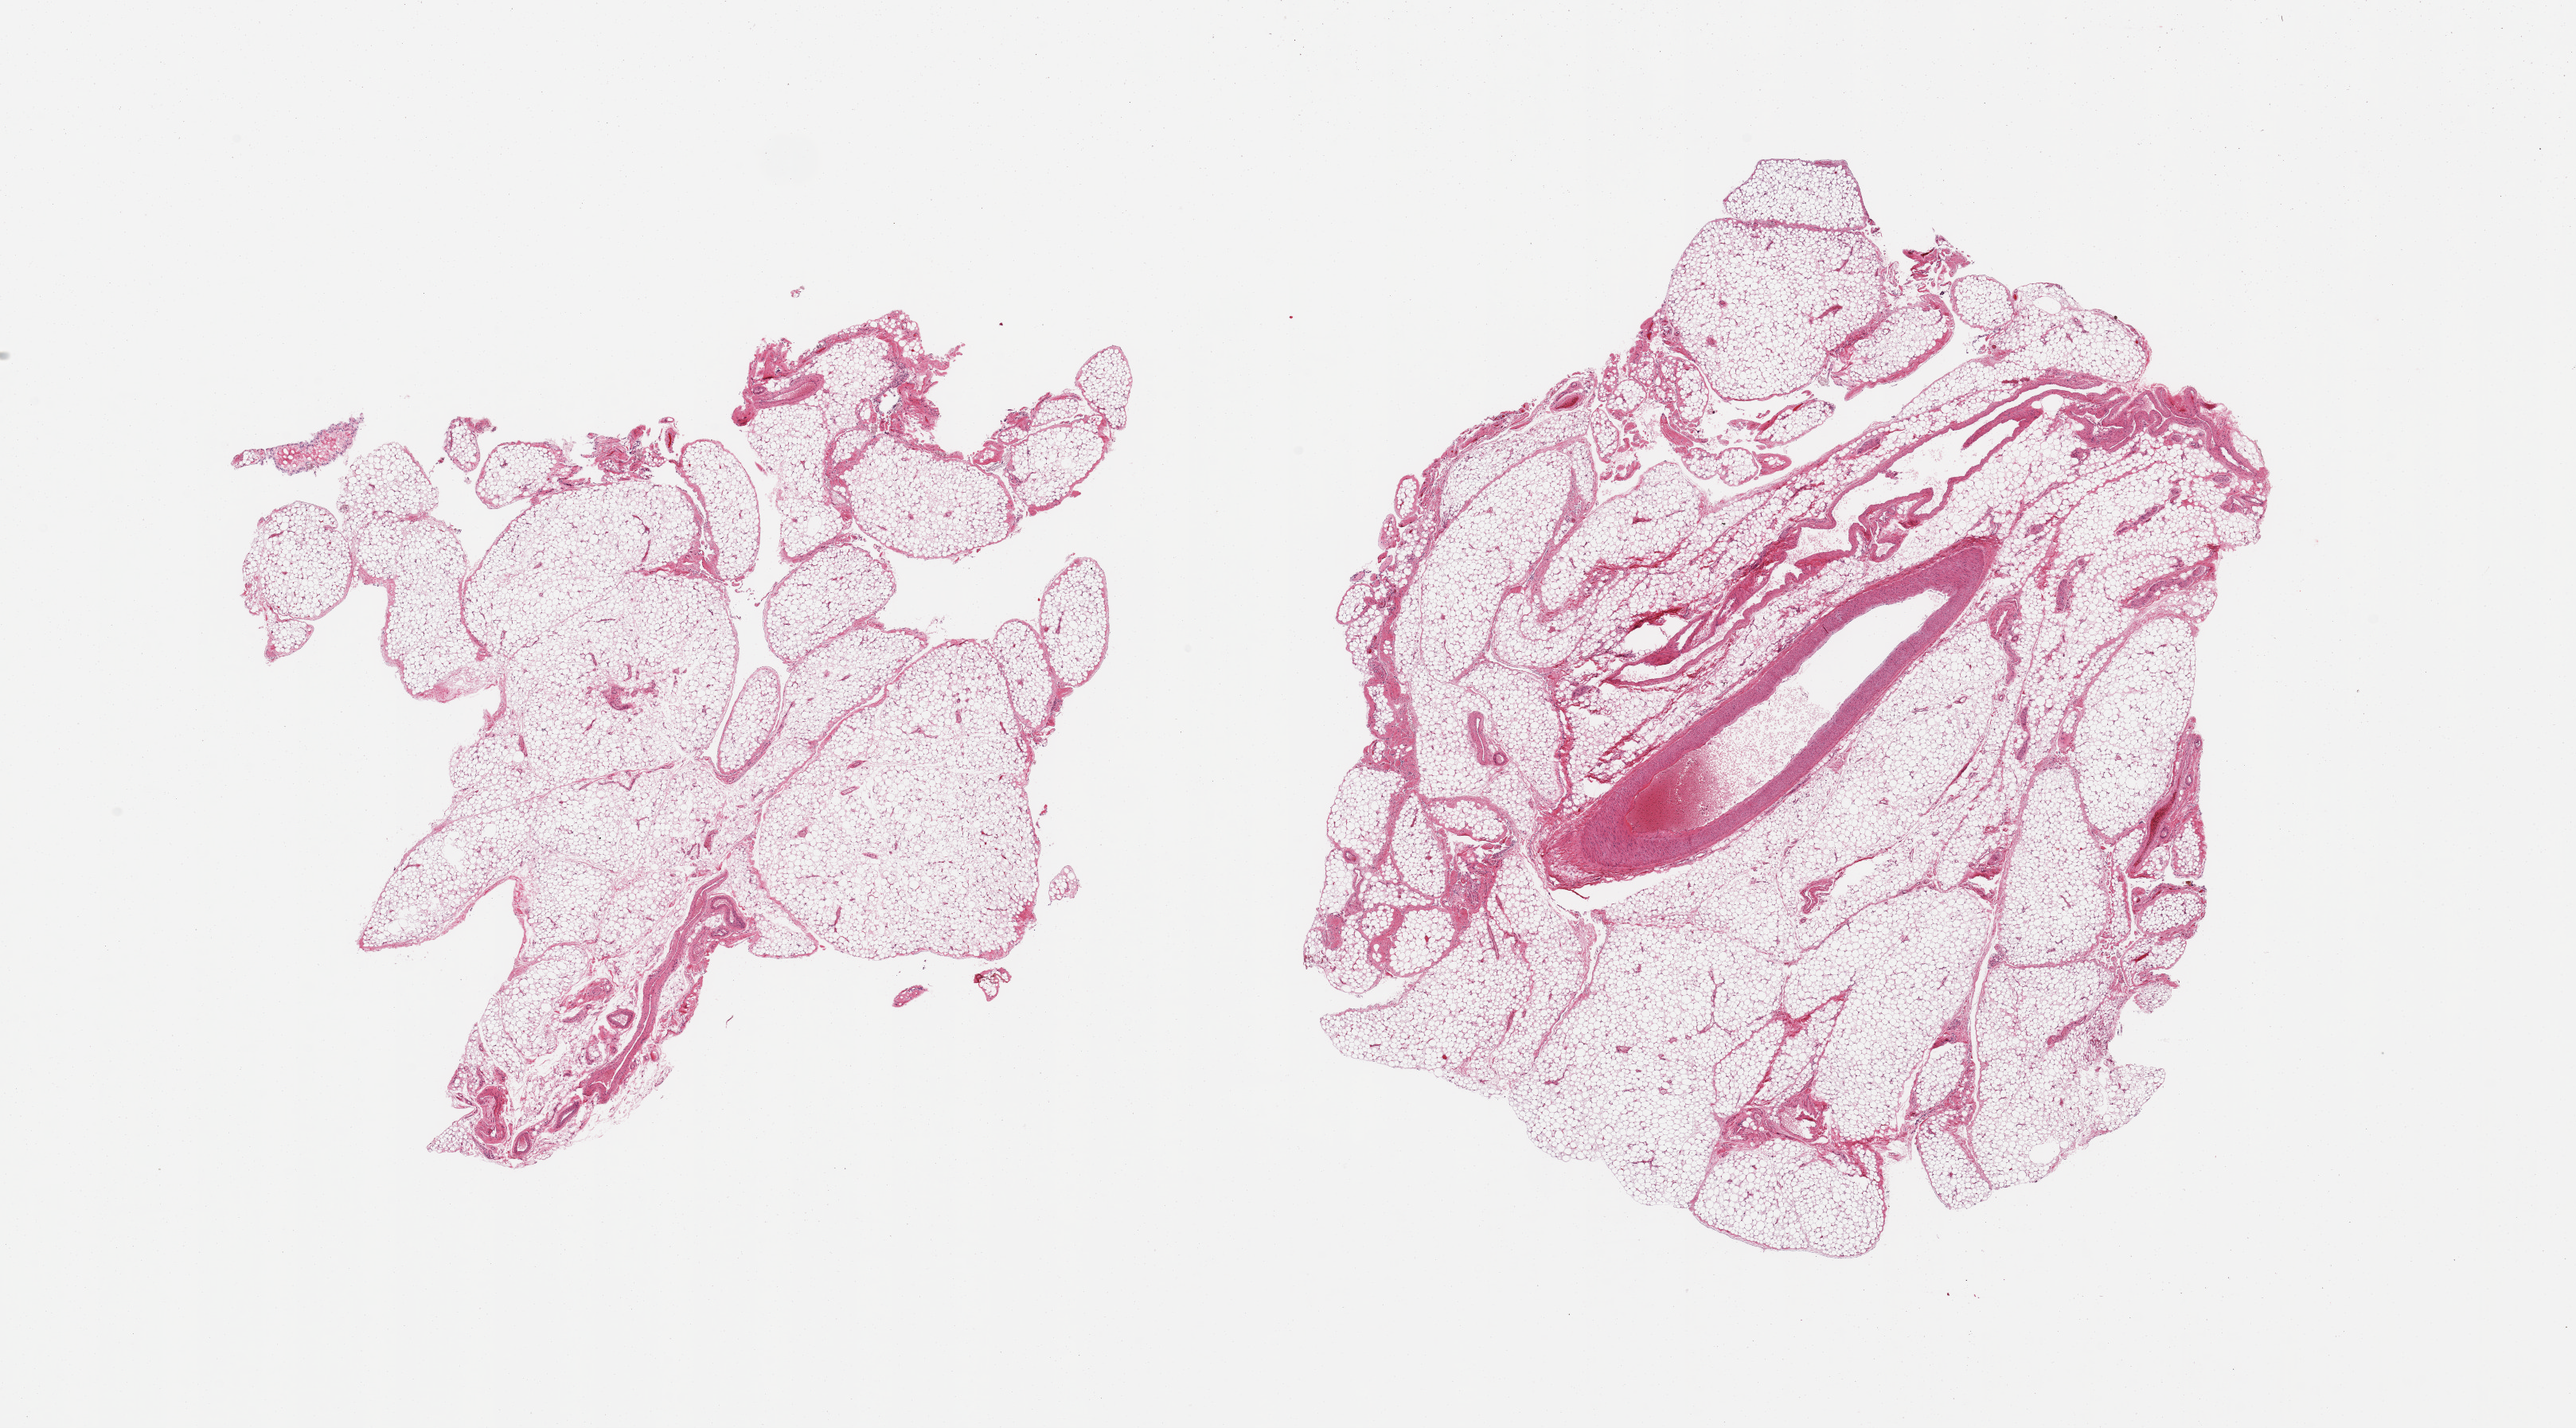
H&E whole-slide image — whole scanned area (about 25.6 x 14.2 mm, acquisition: 20x scan) shown as a low-resolution overview. PAXgene-fixed paraffin-embedded (PFPE) section. Target tissue: omentum. Tissue donor sample. Donor sex: male.
Review note (as recorded): 2 pieces; lobulated mature adipose tissue; one piece contains larger vessel.